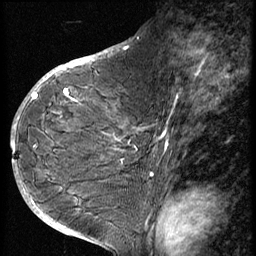
Breast MRI (dynamic contrast-enhanced), one sagittal slice; position 31 of 56 along the scan axis; 3 images stored at this slice position (order not interpretable as contrast timing); 1.5 T; TE 4.2 ms, TR 9 ms; 256 × 256 image matrix, field of view 180 × 180 mm. Patient: female, 49 years. From the clinical record (not read from this slice): setting: breast cancer imaged before/during neoadjuvant chemotherapy; receptor status: HER2-positive.
Structures marked on this image (semi-automatically segmented with operator editing):
- analysis volume of interest (the breast-tissue region the enhancement analysis was run in; not a lesion): bounding box <37,85,131,207> (left, top, right, bottom; pixels)
- tumour enhancement mask (voxels above the 140 % enhancement threshold inside the analysis volume of interest): <37,89,68,97>